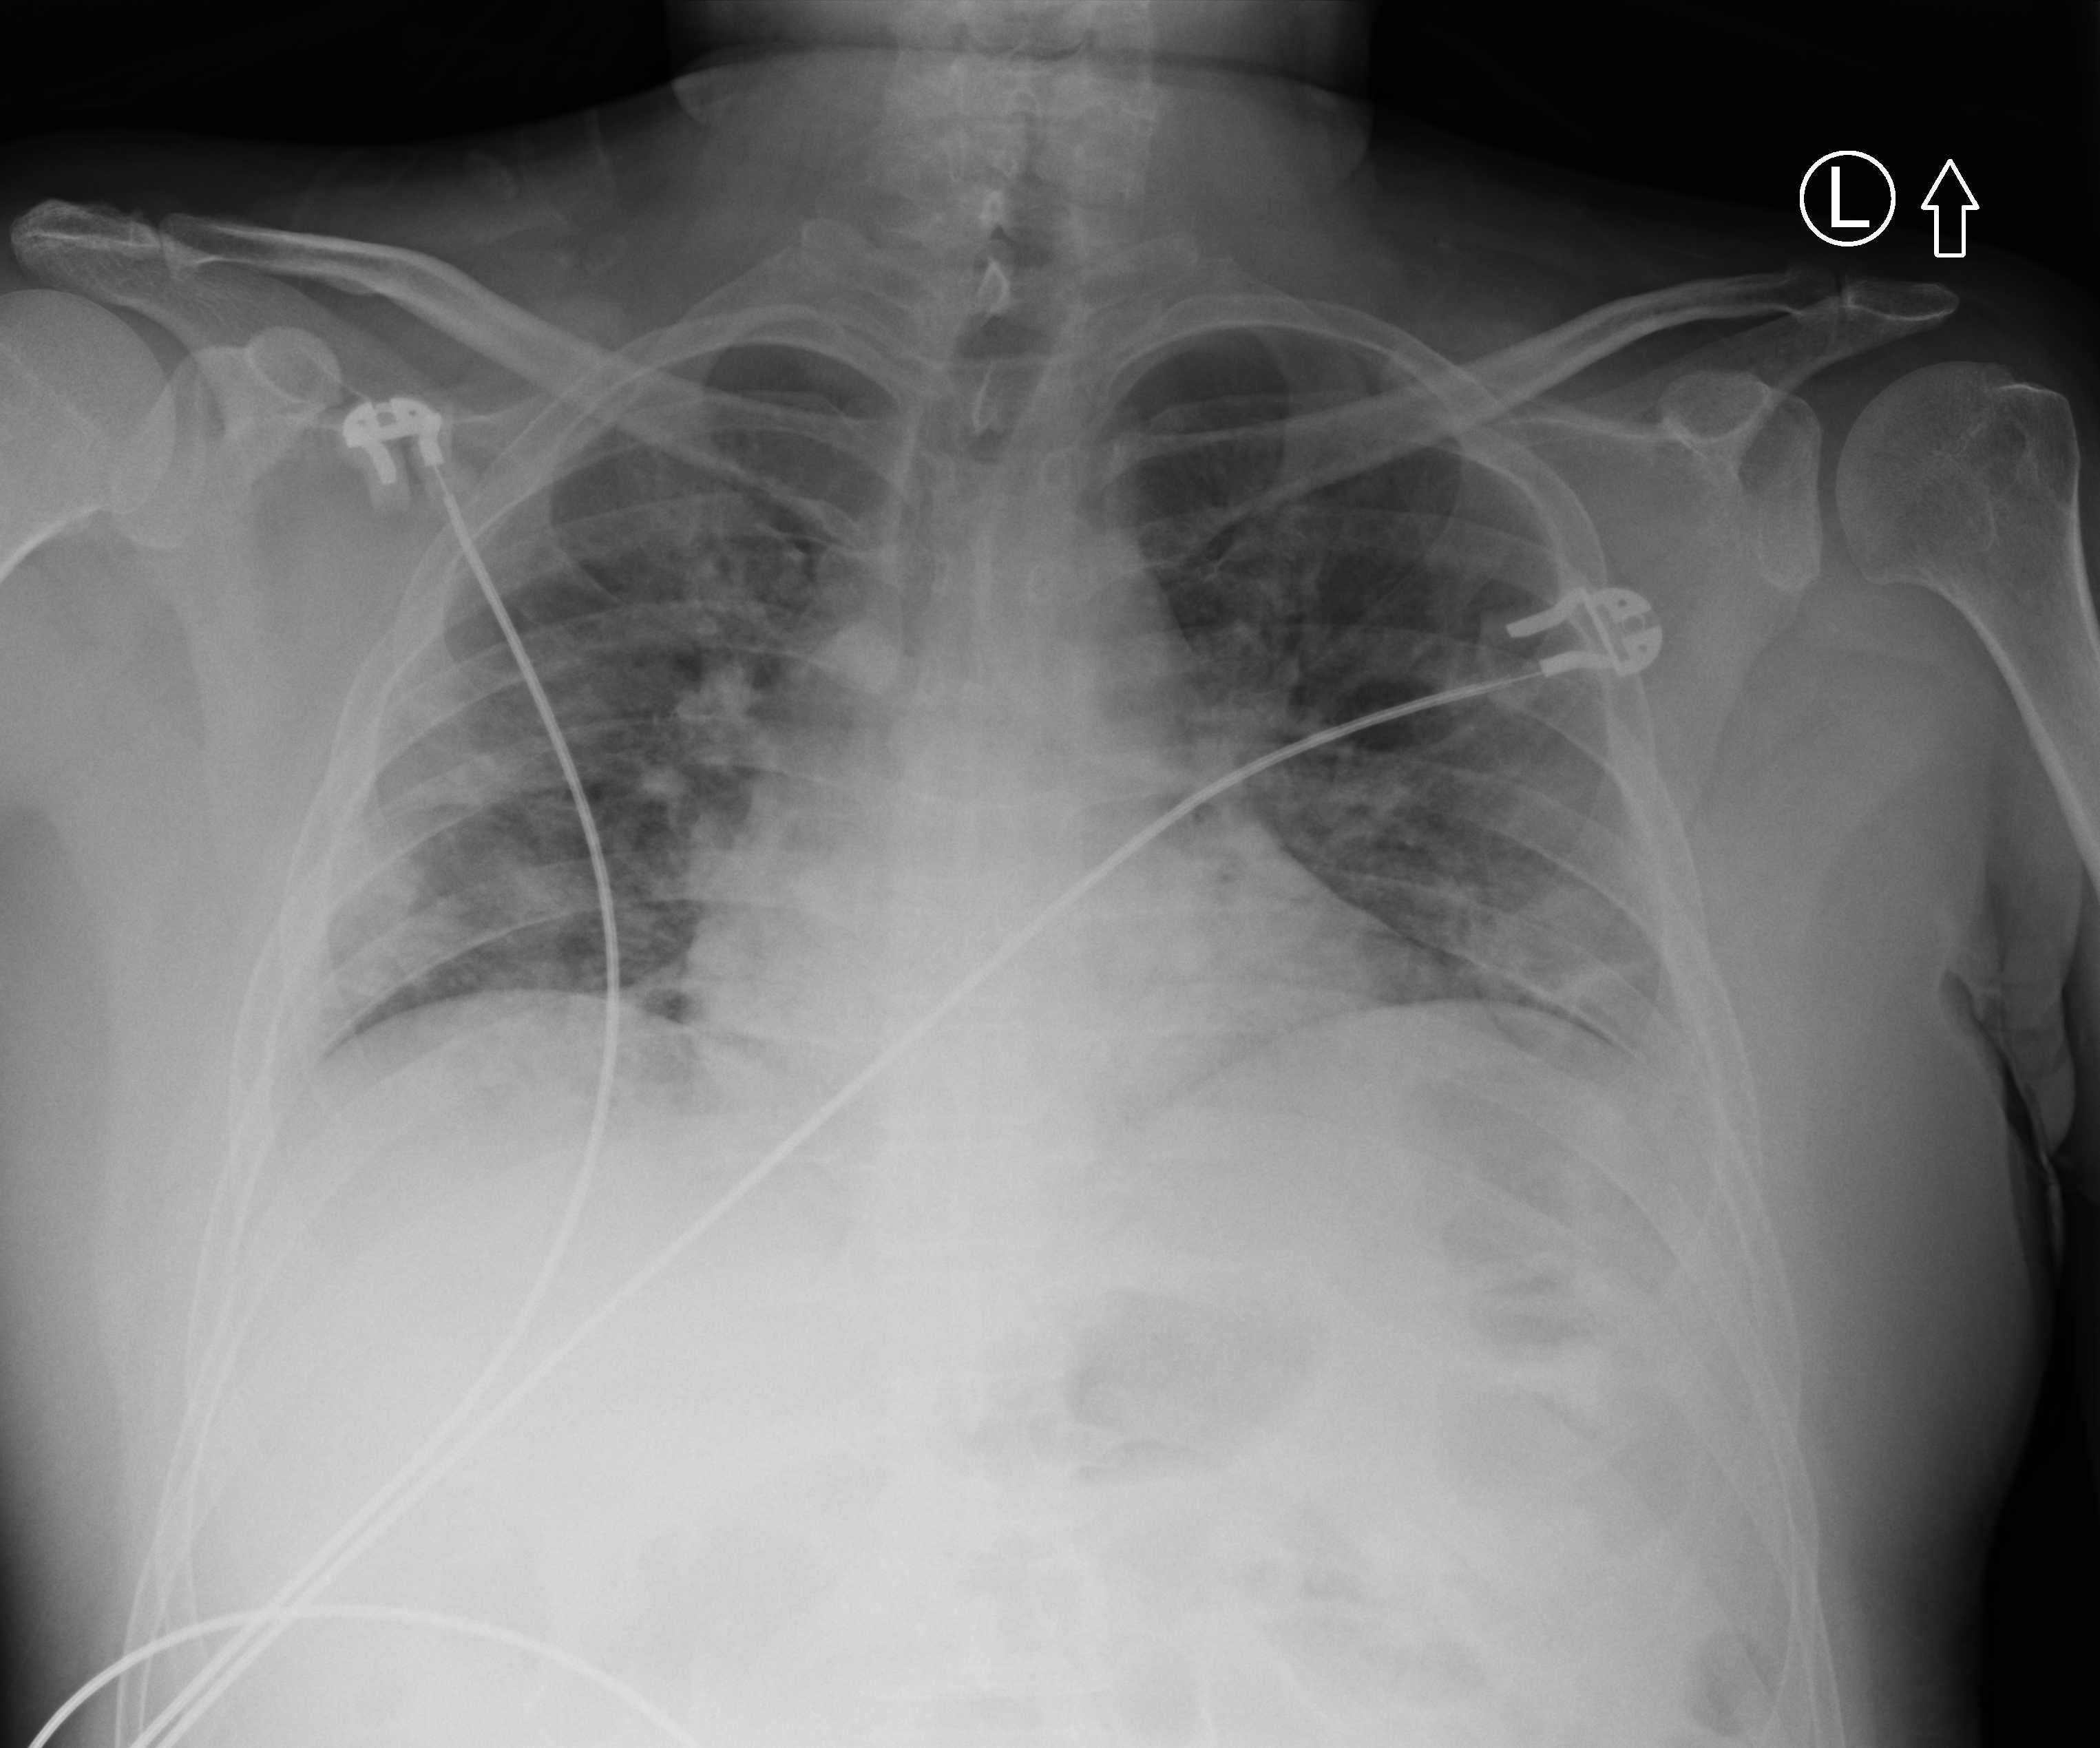
Bedside chest radiograph (computed radiography). Male patient hospitalised with COVID-19, age 18–59 years.
Admission-level facts for this patient (not findings on this image; timing relative to this image not recorded):
- admitted to intensive care during this hospital stay: no